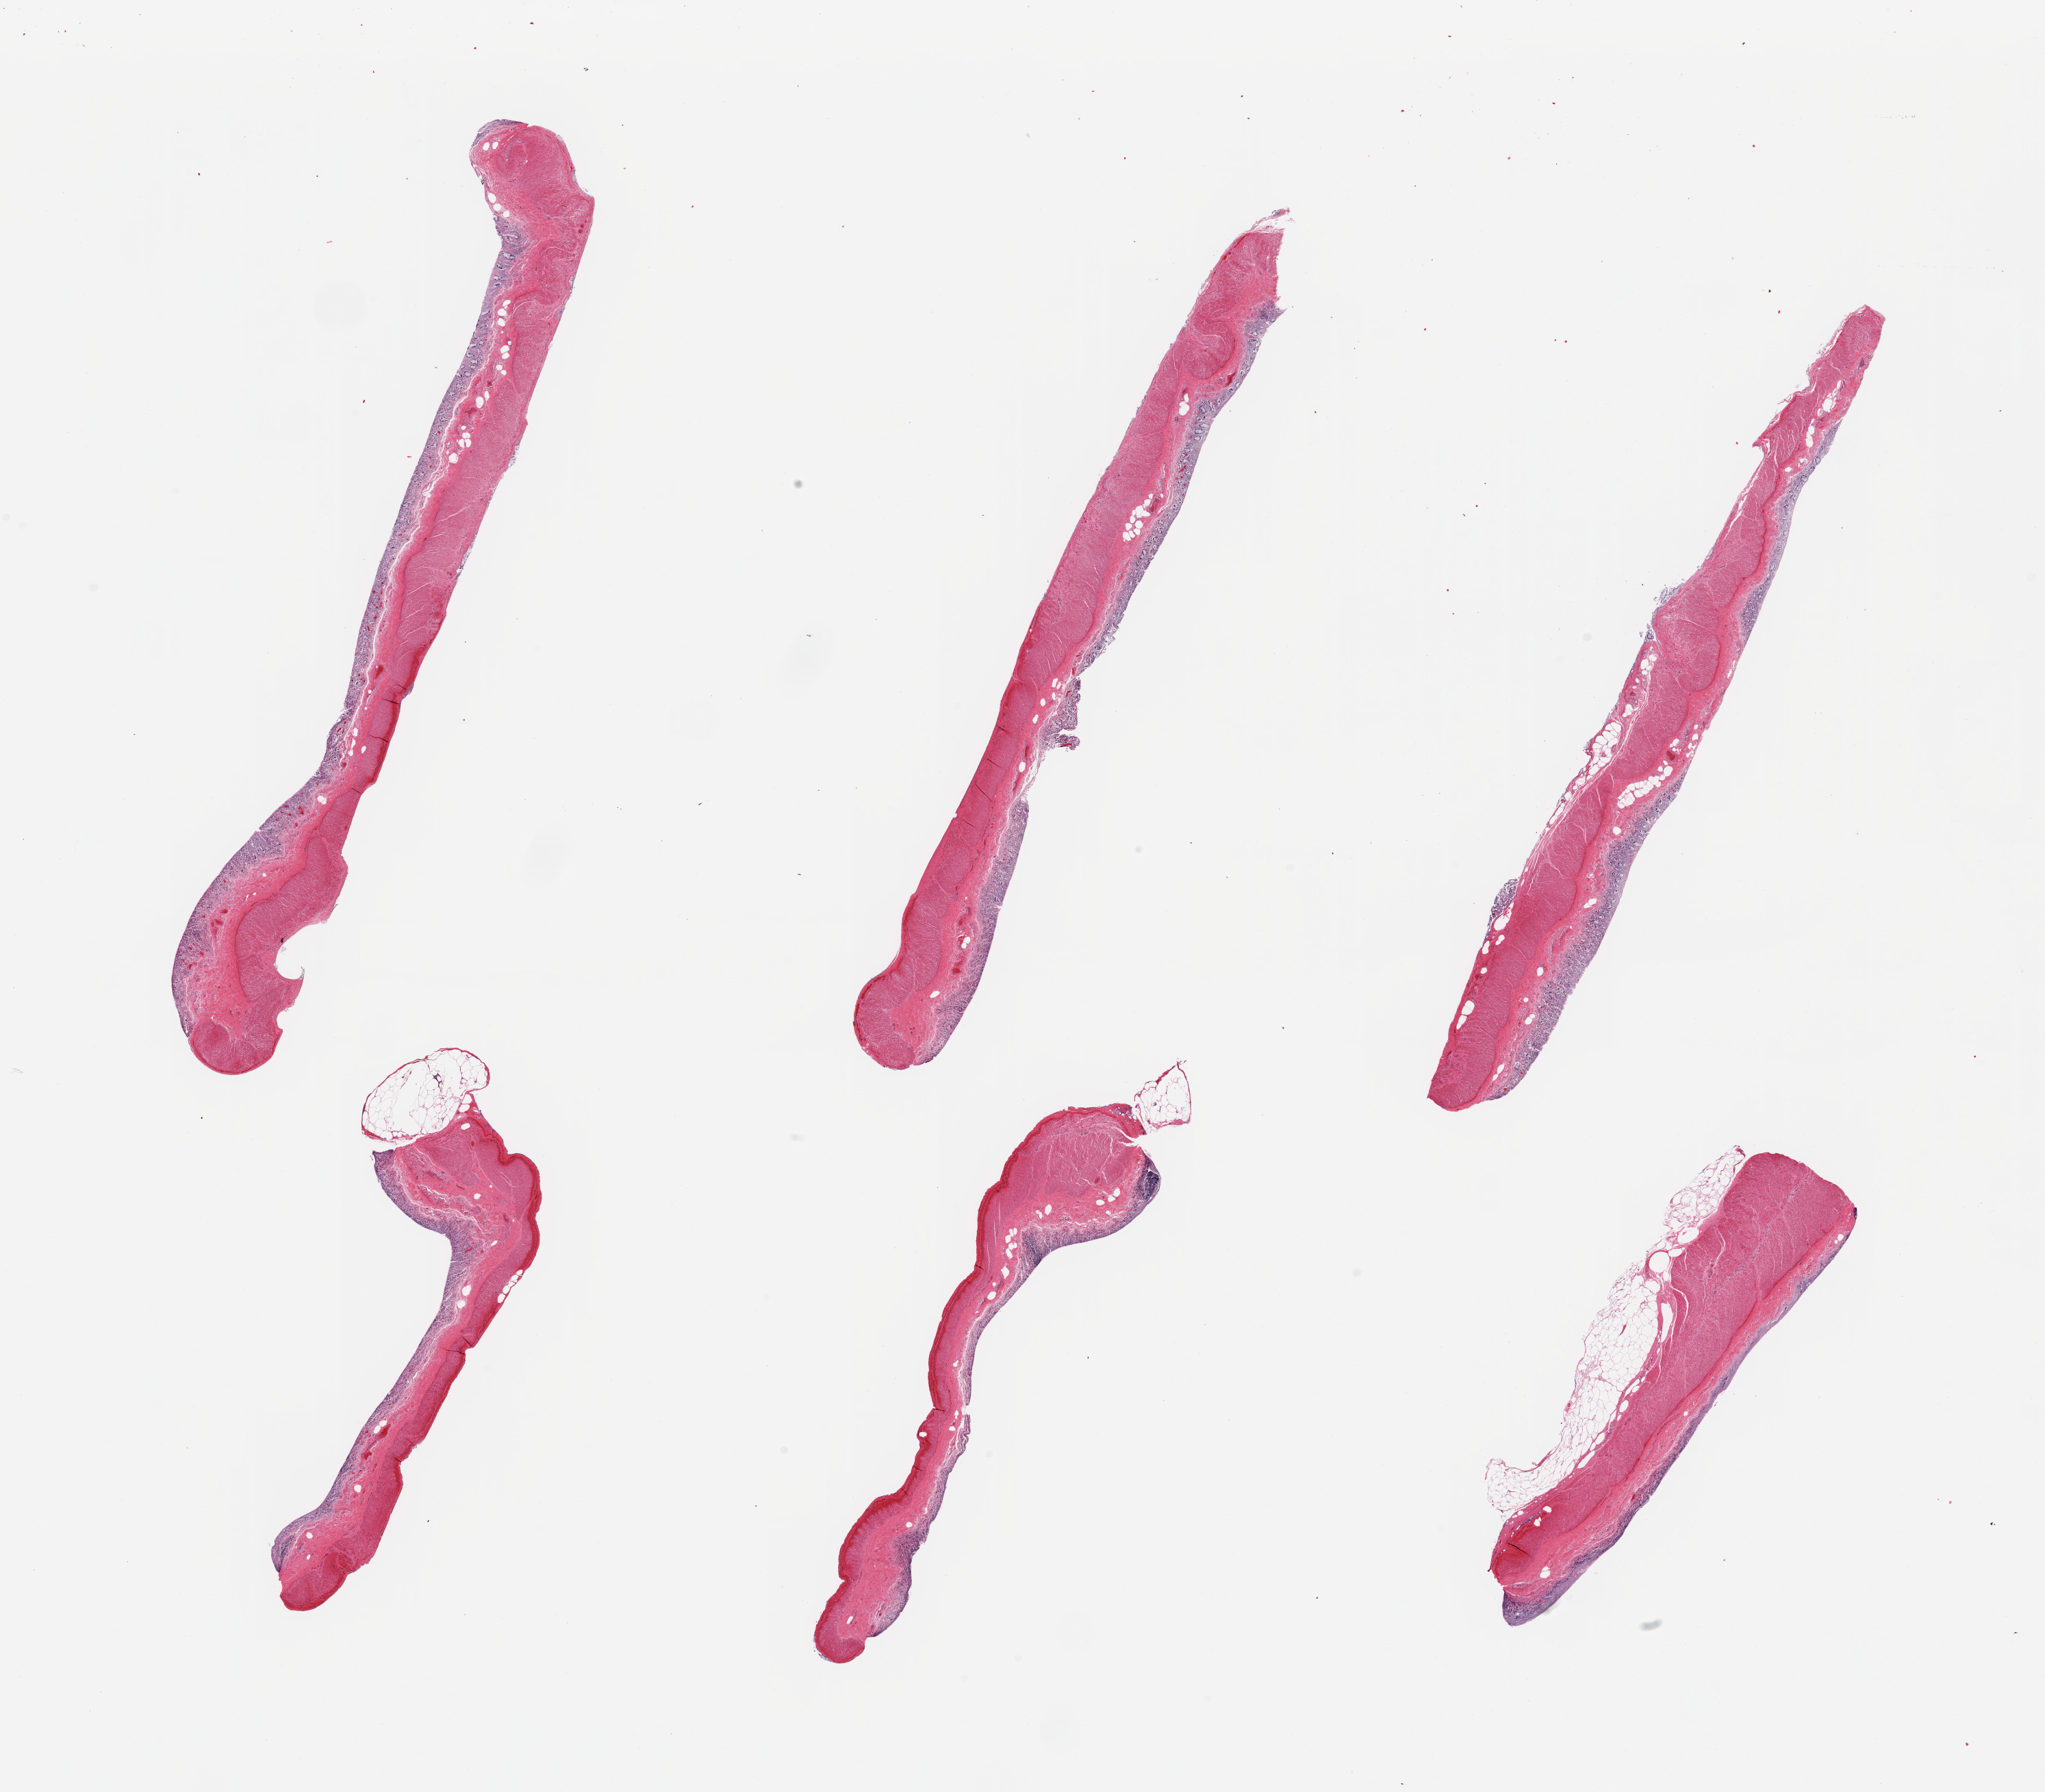
Haematoxylin and eosin whole-slide image, brightfield, whole scanned area (about 23.6 x 20.7 mm, acquisition: 20x scan) shown as a low-resolution overview. PAXgene-fixed, paraffin-embedded tissue. Target tissue: transverse colon. Donor tissue sample. Donor: male.
Reviewer comment on this tissue sample: 6 pieces, glandular mucosa up to ~0.3mm, but totally autolyzed/sloughed.